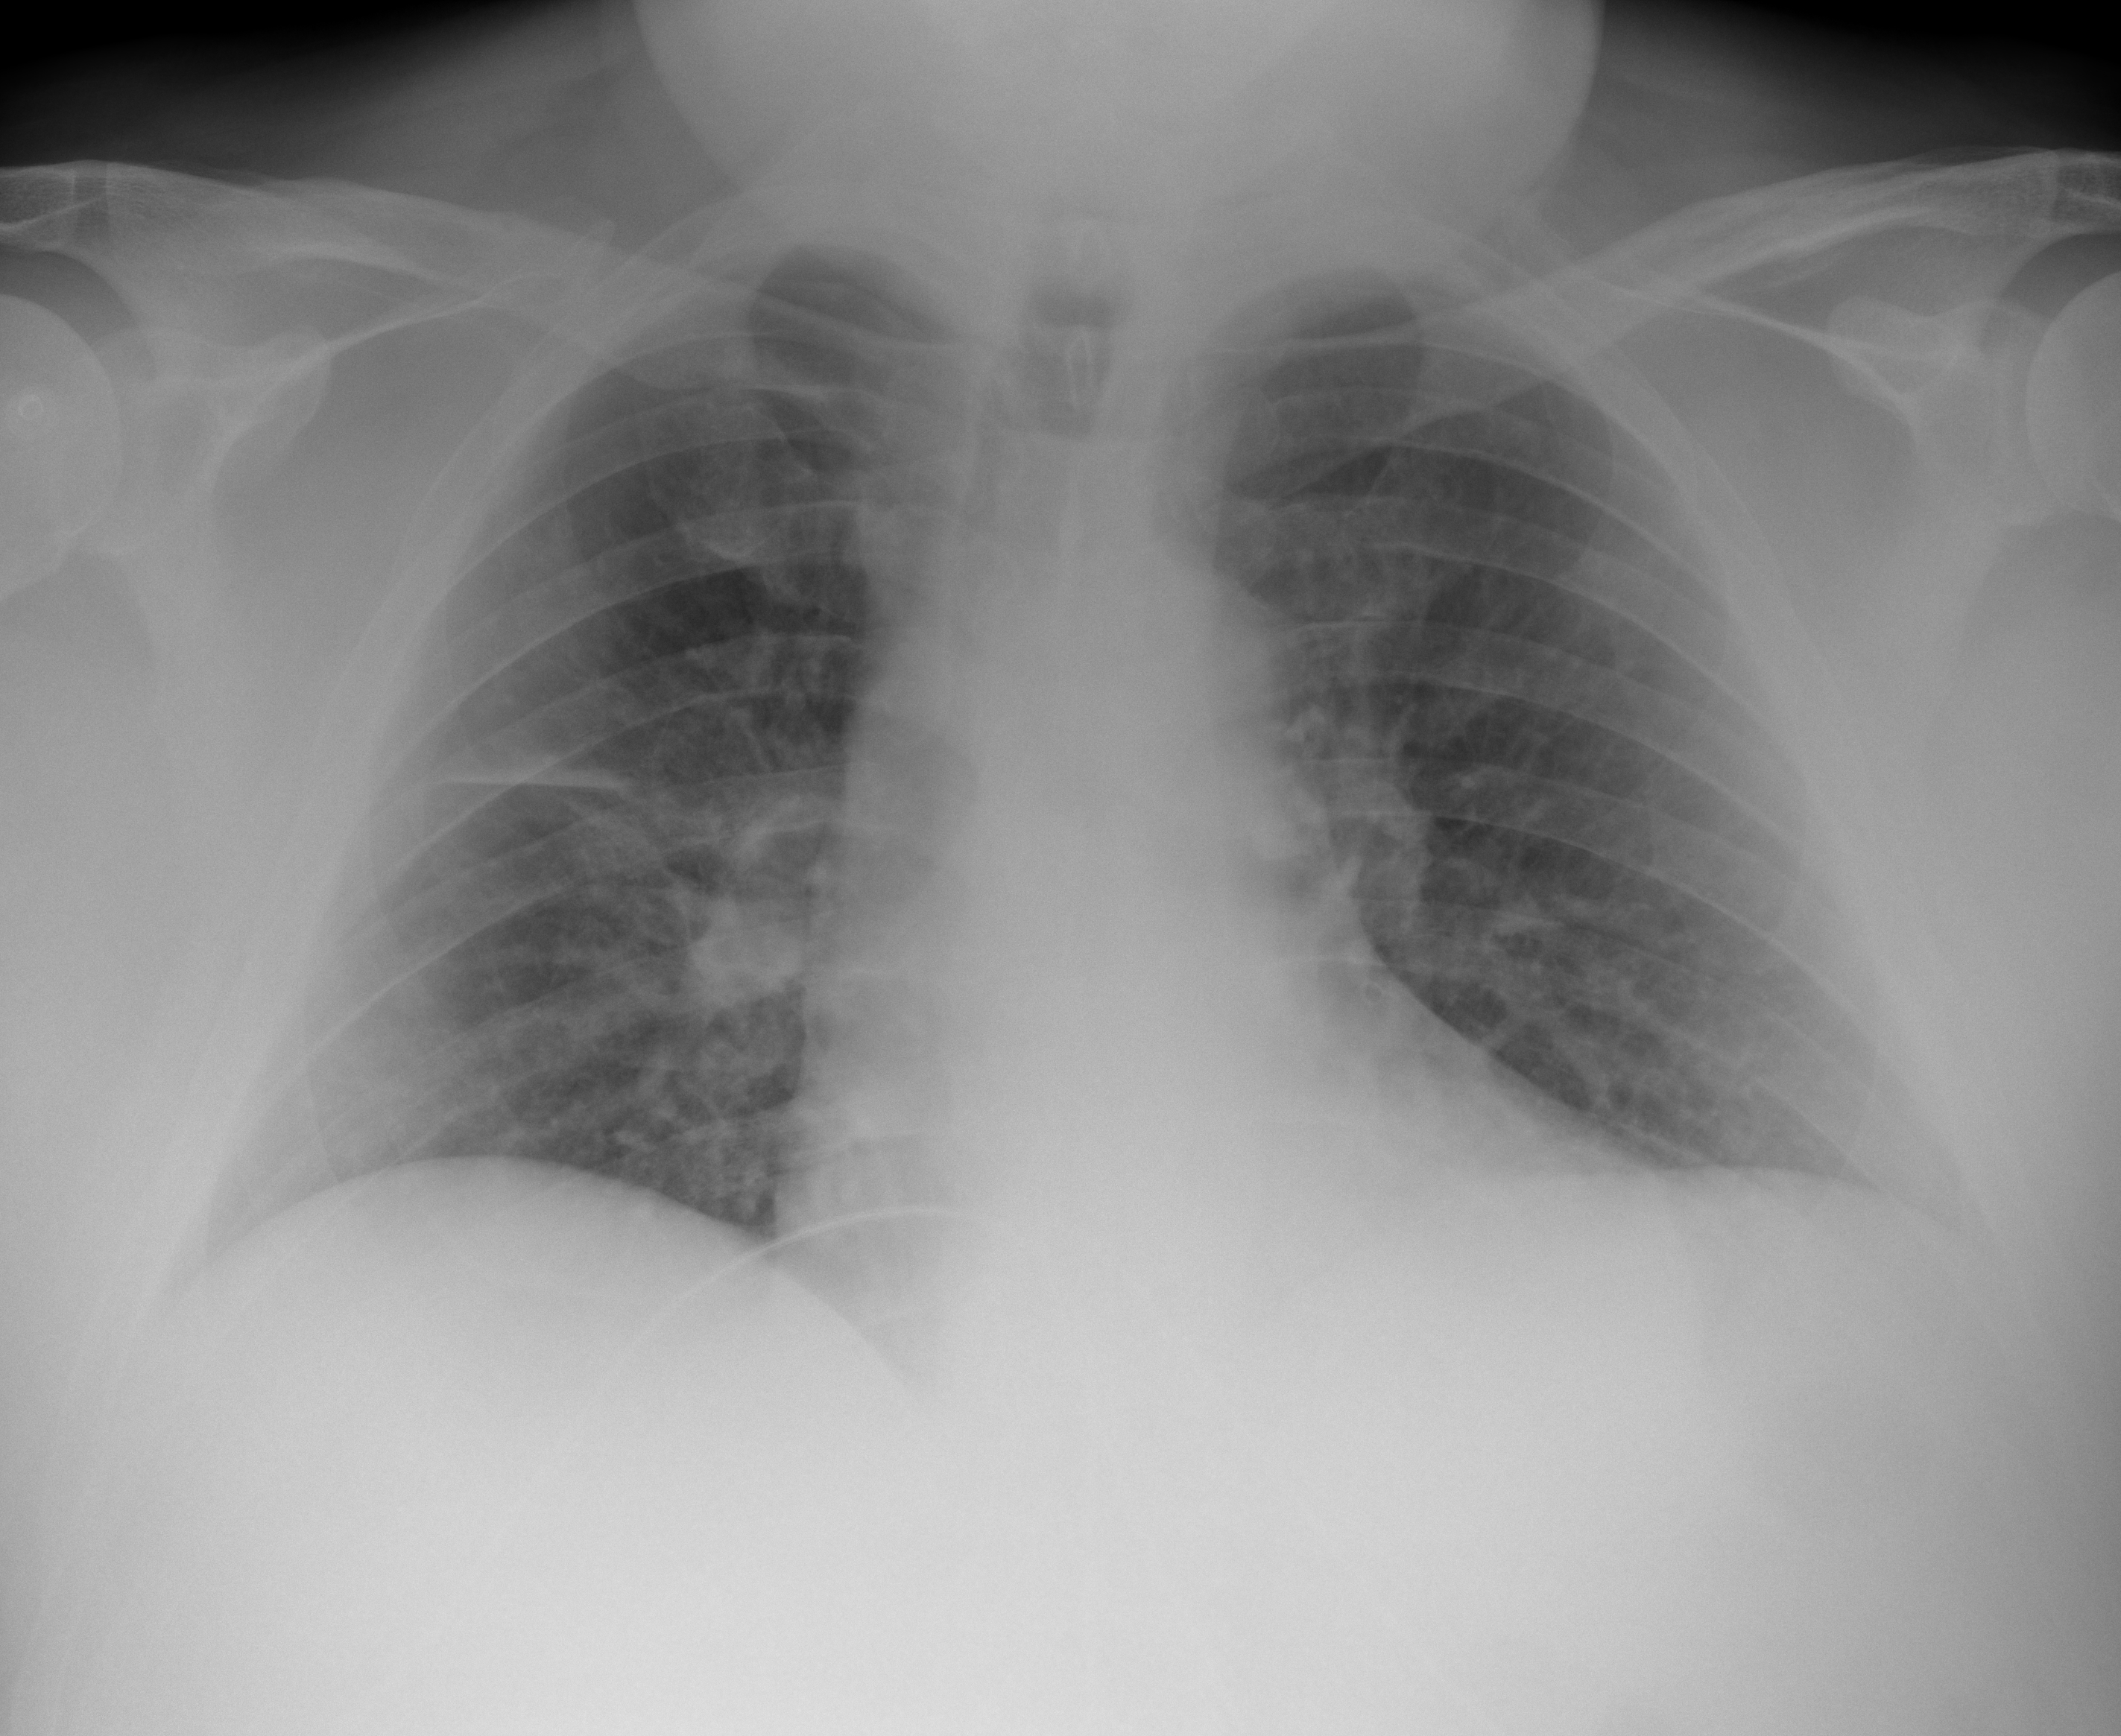
Portable chest radiograph, AP projection. Male patient, age 61 years; imaged 0 days after the COVID-19 diagnosis.
Radiologist's key findings for this exam: Right upper lobe atelectasis.